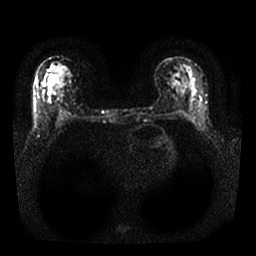
Breast MRI, one axial slice; position 16 of 25 along the scan axis; diffusion-weighted series; image 2 of 4 stored at this slice position (different b-values; order by instance number); 1.5 T; 256 × 256 image matrix. Female patient.
Structures marked on this image (expert manual segmentation):
- tumour on diffusion-weighted imaging: bounding box [x1, y1, x2, y2] px = [48, 77, 56, 81]